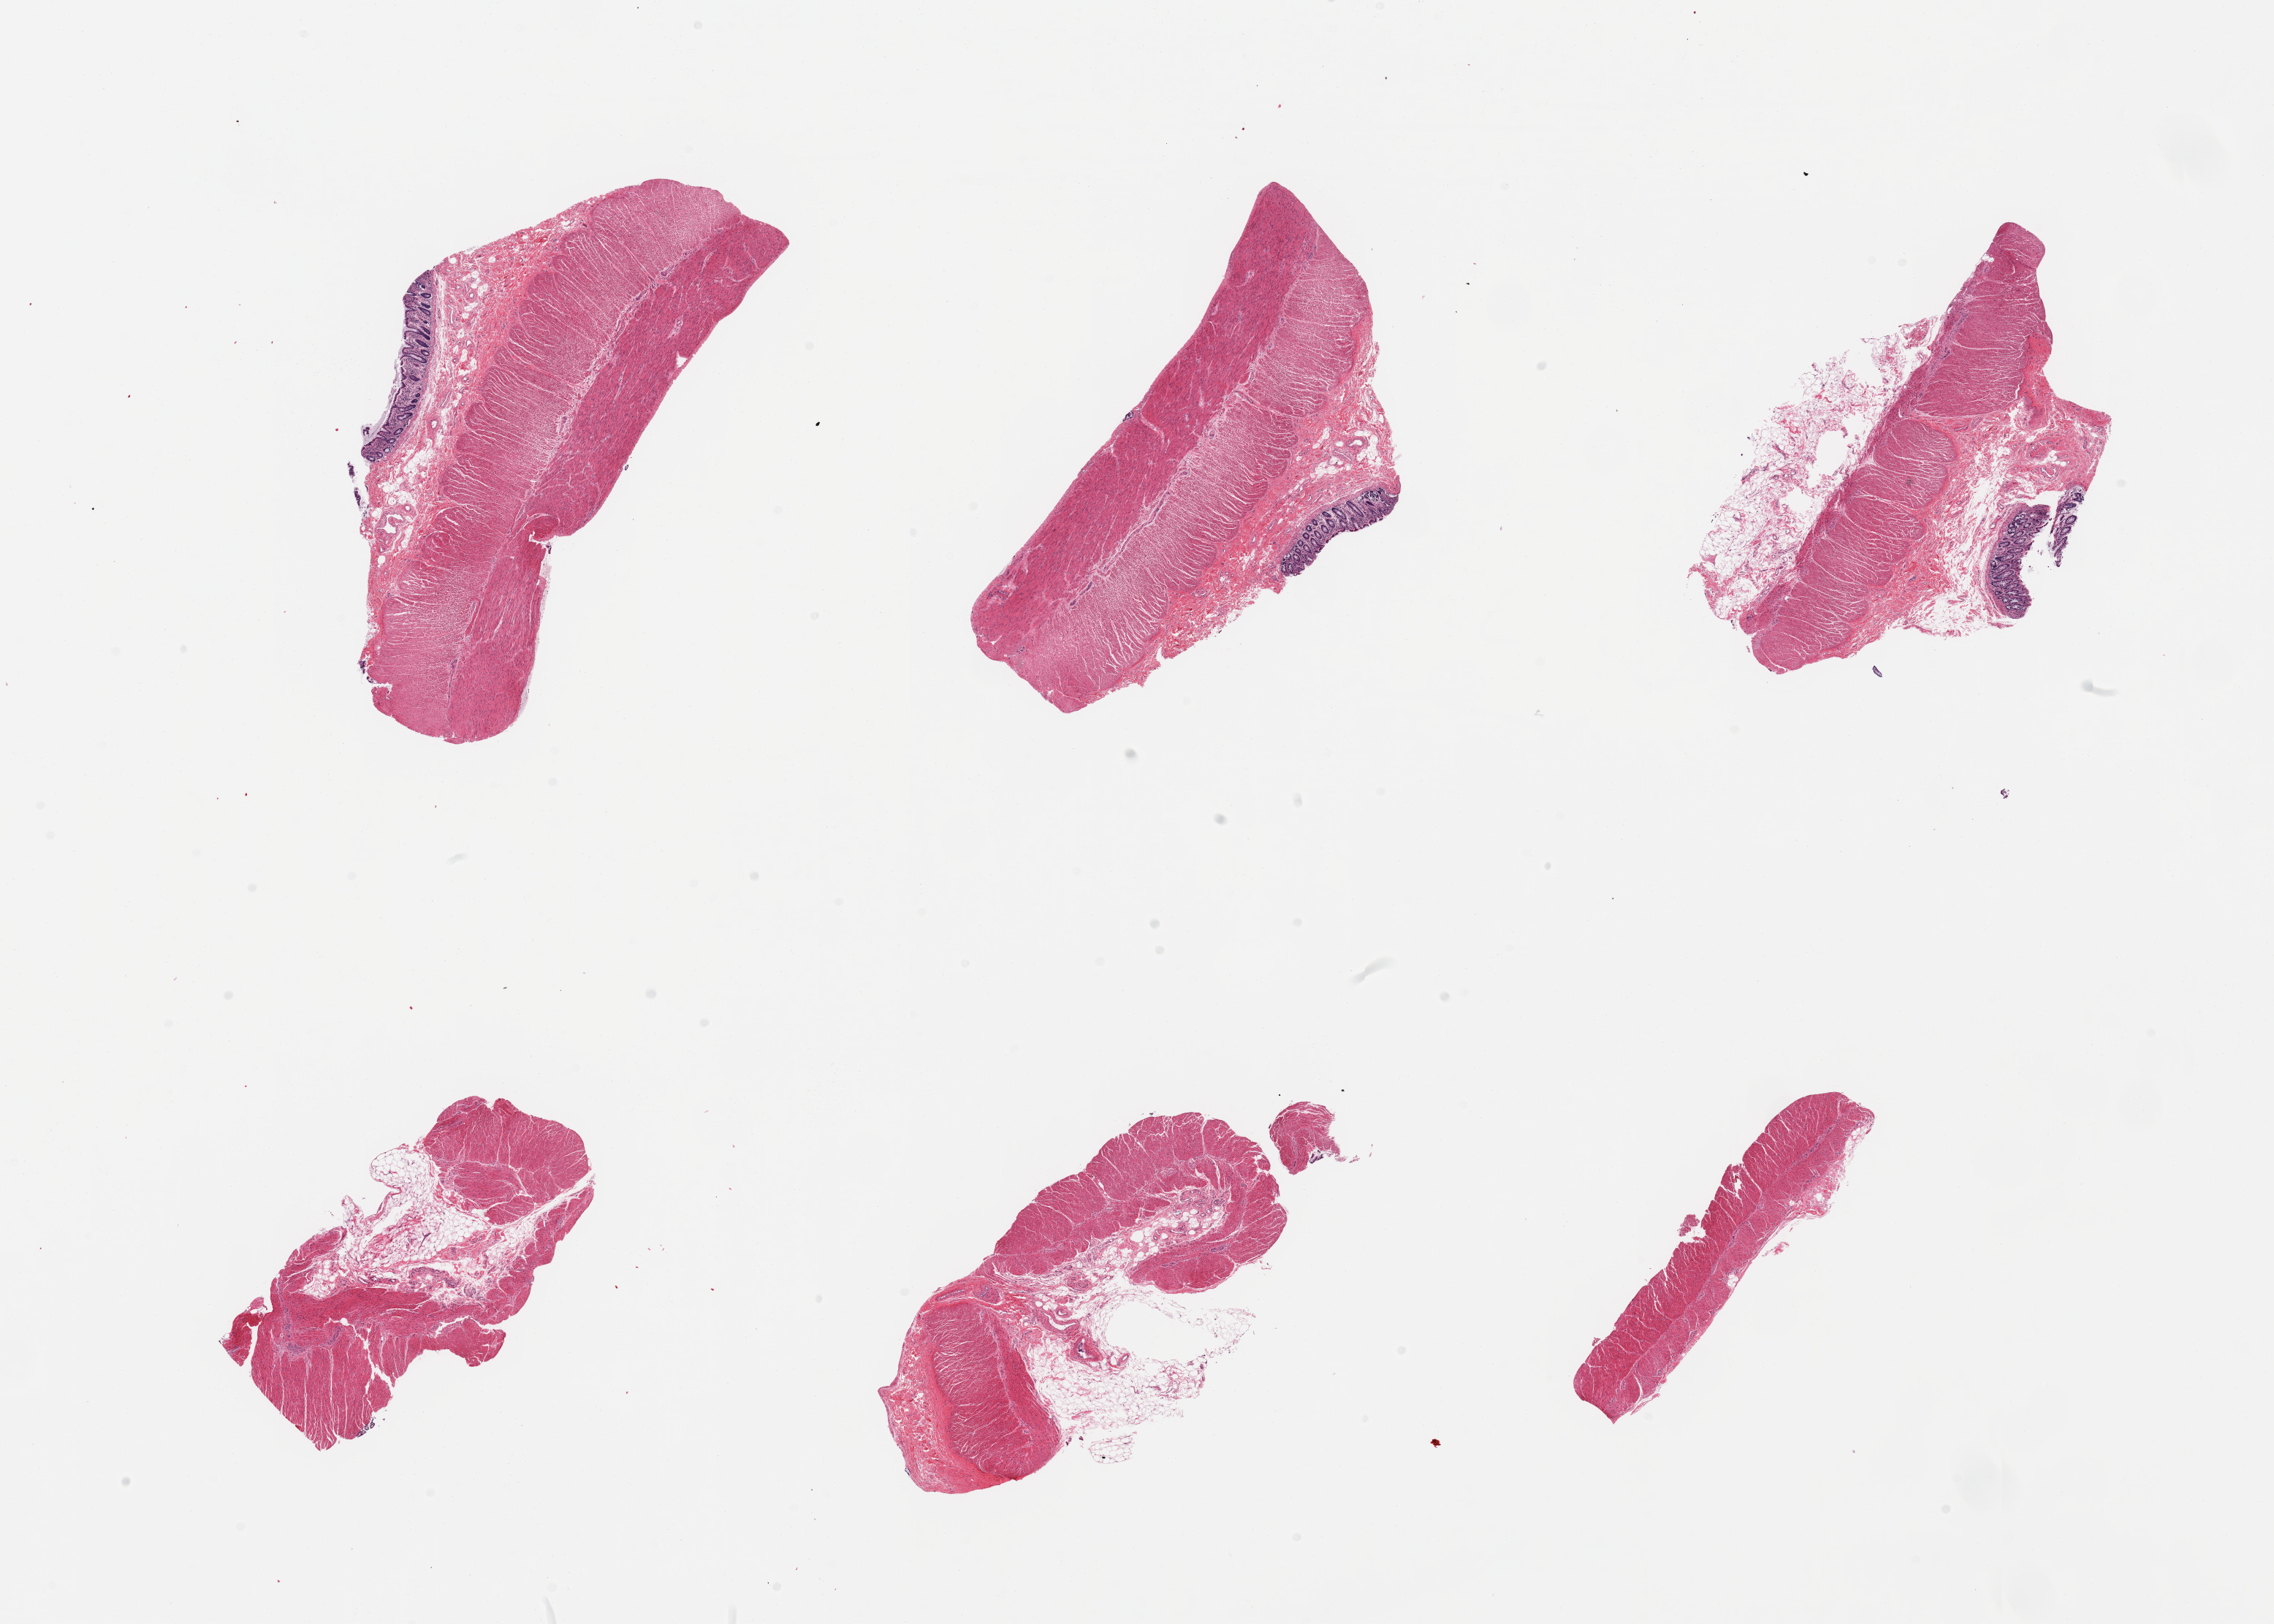
H&E whole-slide image, a low-resolution overview of the entire scanned area, about 24.6 x 17.6 mm. PAXgene-fixed paraffin-embedded (PFPE) section. Section of sigmoid colon (target tissue). Donor tissue sample.
Pathologist's review note for this sample: 6 pieces; 3 include strips of mucosa, ~30% fat also present in several pieces.